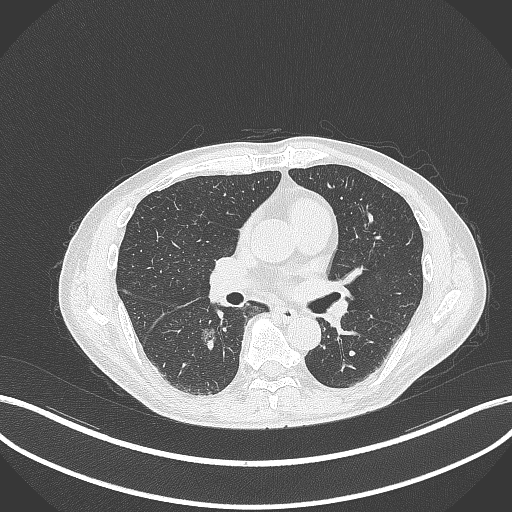
Chest CT, one axial slice. Position 169 of 323 along the scan axis. Reconstruction kernel B70f. Lung window (W 1500 / L -600 HU). 512 × 512 image matrix. Male patient, age 61 years. From the clinical record (not read from this slice): clinical TNM (as recorded): T1c N0 M0.
Annotated regions visible in this slice (rectangle marked by the reading radiologist):
- lung tumour (recorded histology: adenocarcinoma): bounding box [x1, y1, x2, y2] px = [198, 325, 219, 347]